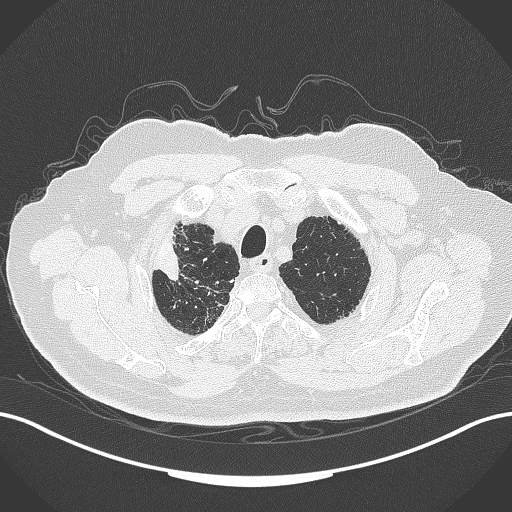
Chest CT, one axial slice; position 312 of 389 along the scan axis; reconstruction kernel B70f; 120 kVp; lung window (W 1500 / L -600 HU); 1 mm slice thickness; 512 × 512 image matrix. Male patient, age 72 years. From the clinical record (not read from this slice): clinical TNM (as recorded): T1a N0 M0.
Structures marked on this image (rectangle marked by the reading radiologist):
- lung tumour (recorded histology: squamous cell carcinoma): bounding box (x1, y1, x2, y2) in pixels: (151, 229, 189, 289)